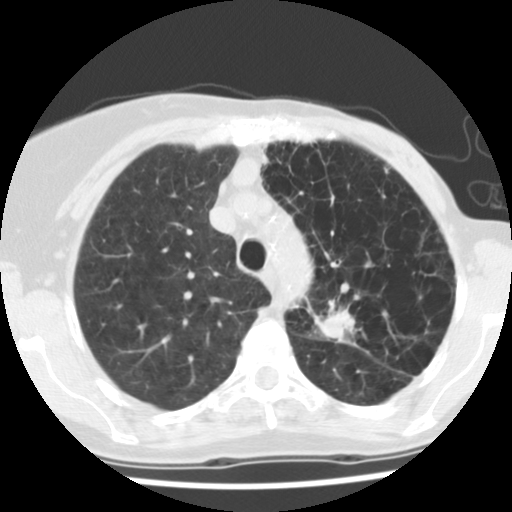
Low-dose screening chest CT, one axial slice. Slice 97 of 128 in the series (ordered by position). Reconstruction kernel STANDARD. 140 kVp. Lung window (W 1500 / L -600 HU). 2.5 mm slice thickness. 512 × 512 image matrix, field of view 290 × 290 mm.
Structures marked on this image (outlined manually by an expert reader):
- lesion 1 (tumor, upper lobe of left lung): bounding box [x1, y1, x2, y2] px = [314, 307, 357, 342]